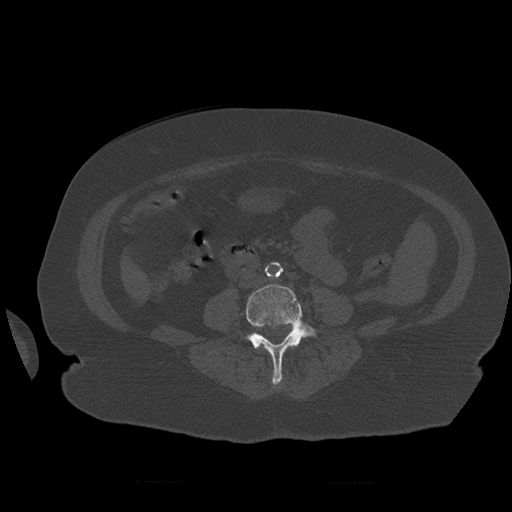
CT including the spine, one axial slice. Position 205 of 399 along the scan axis. 120 kVp. Bone window (W 1800 / L 400 HU). 512 × 512 image matrix, field of view 404 × 404 mm. Patient age 81 years. From the clinical record (not read from this slice): primary cancer: renal; vertebrae with lytic lesions (as recorded): L1.
Annotated regions visible in this slice (semi-automatically segmented with operator editing):
- L4 vertebra: bounding box (x1, y1, x2, y2) in pixels: (246, 284, 317, 385)